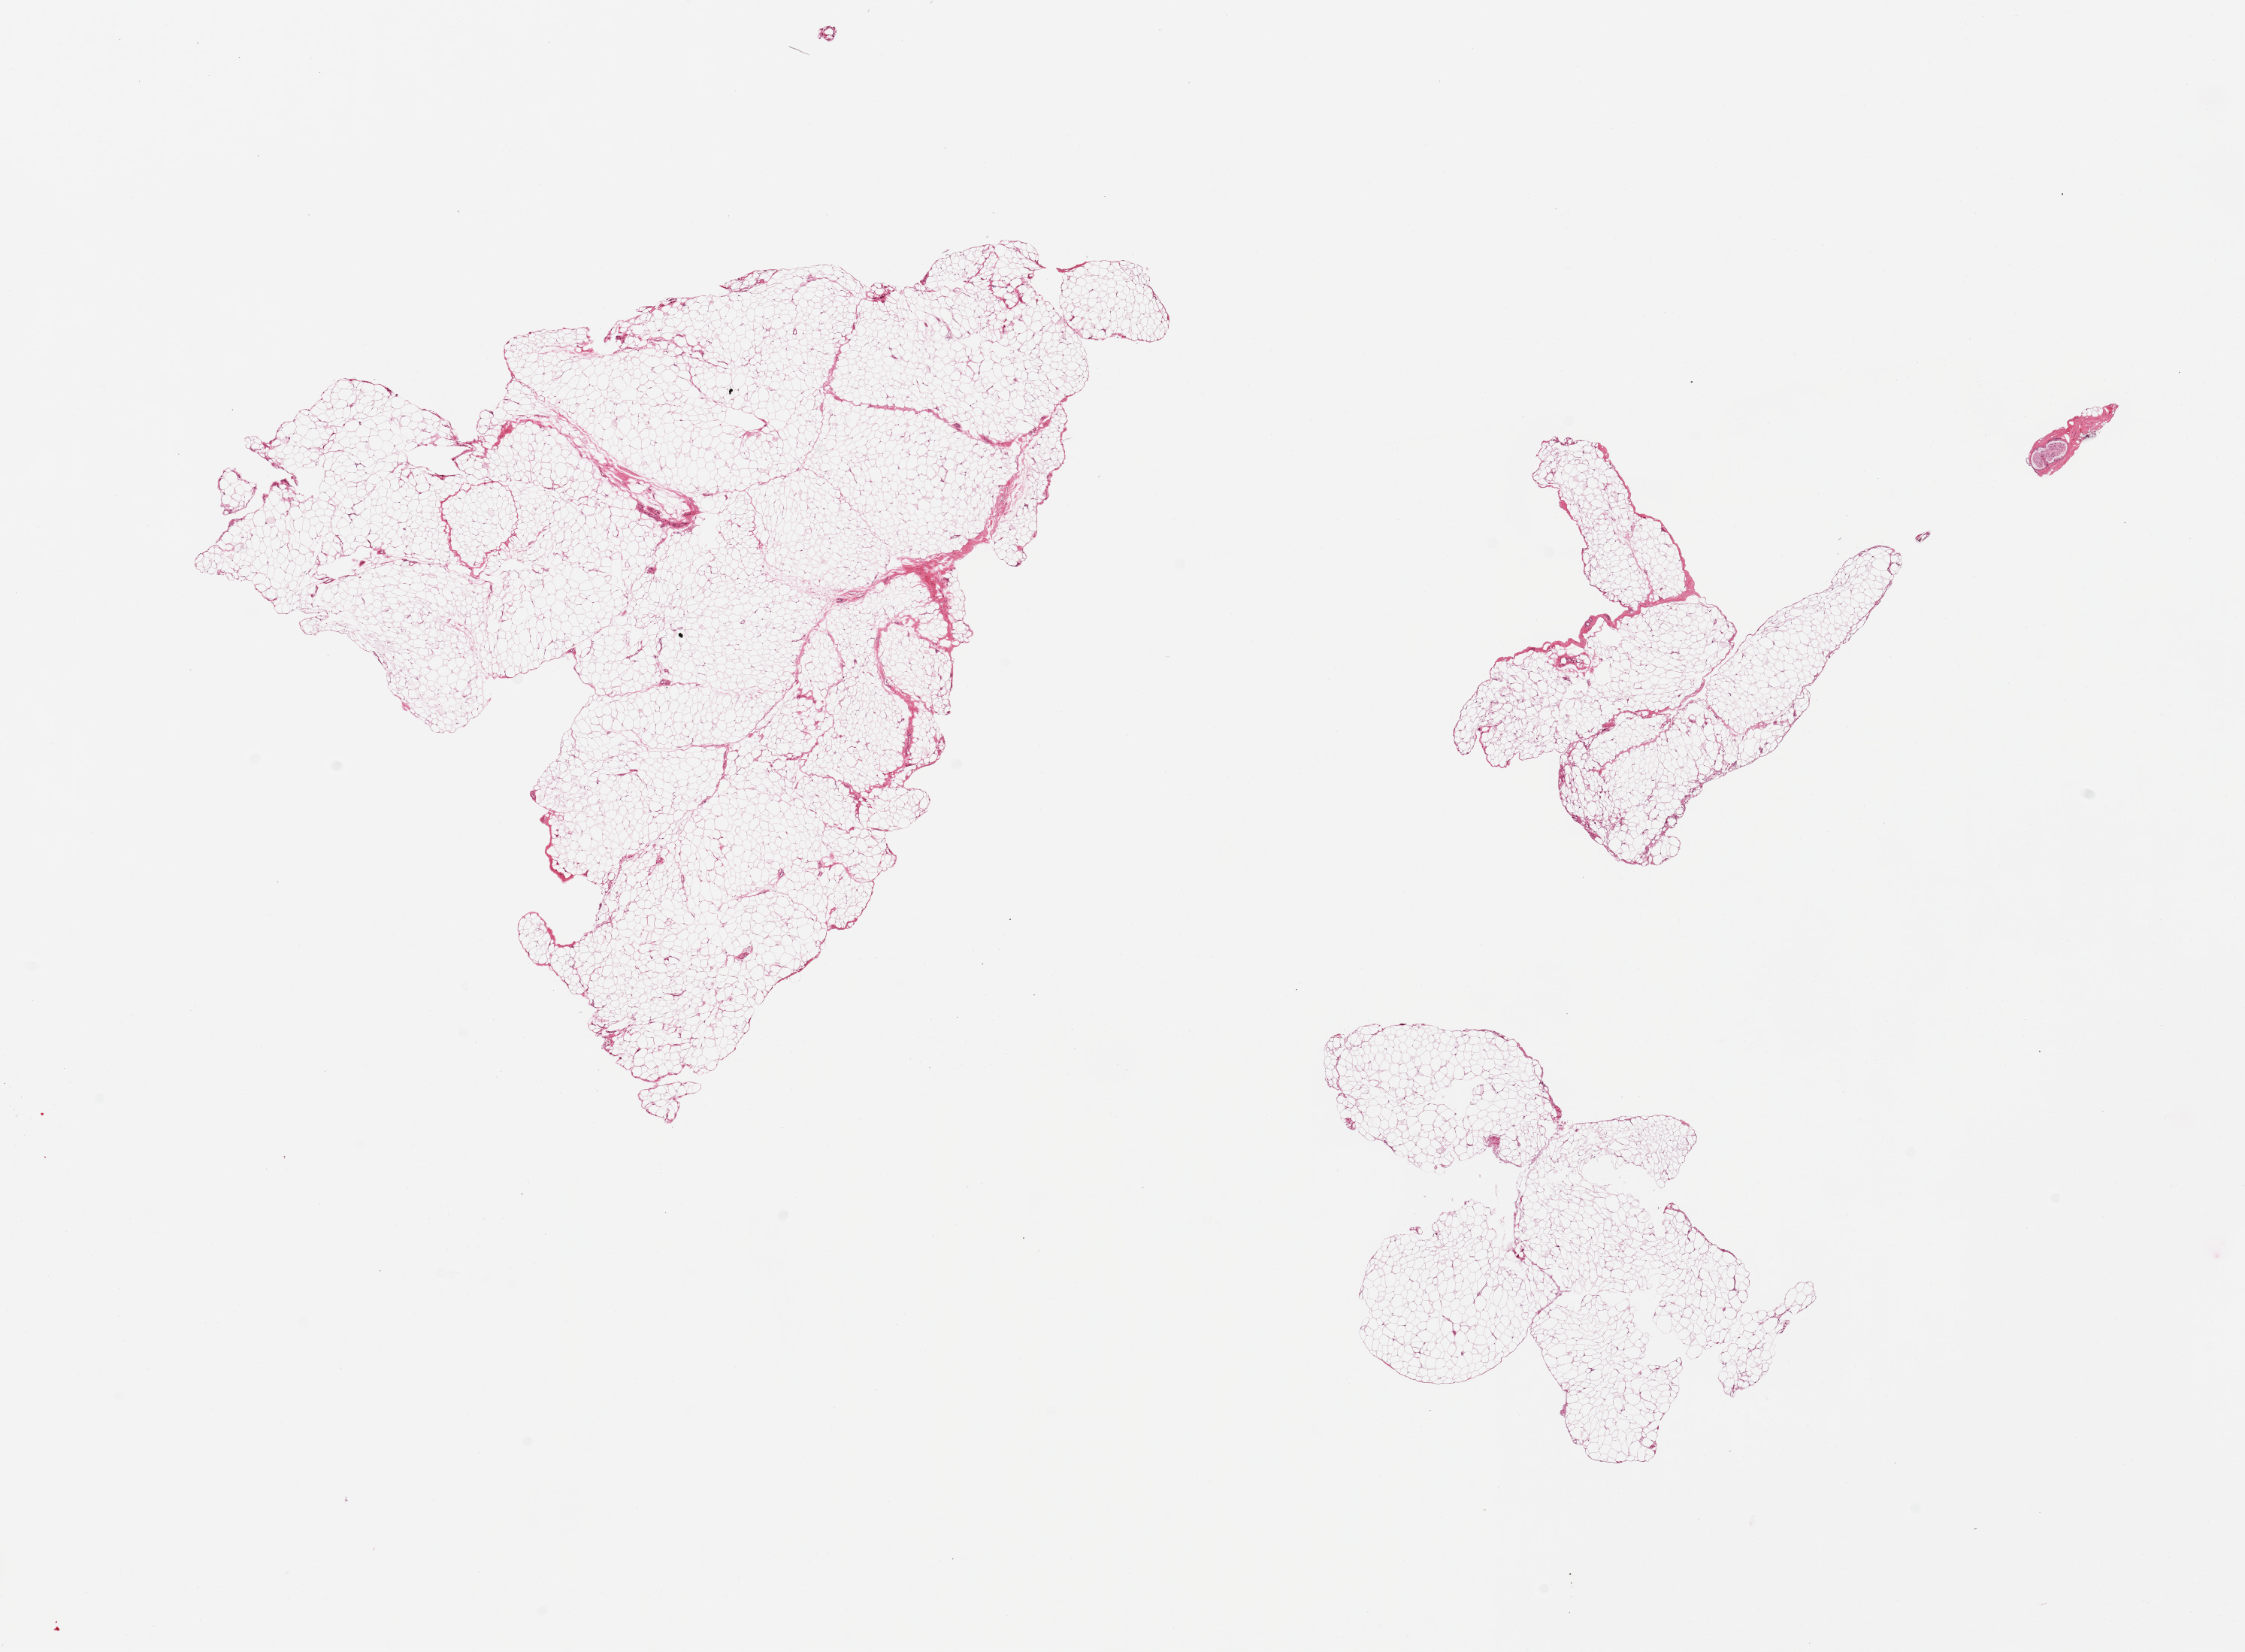
Haematoxylin and eosin whole-slide image, low-resolution overview of the scanned area, about 23.6 x 17.4 mm (slide scanned at 20x). PAXgene-fixed paraffin-embedded (PFPE) section. Section of adipose tissue (target tissue). Donor tissue sample. Donor: male.
• pathologist's review note for this sample: 2 pieces, minimal fascia/fibrous tissue, good specimens